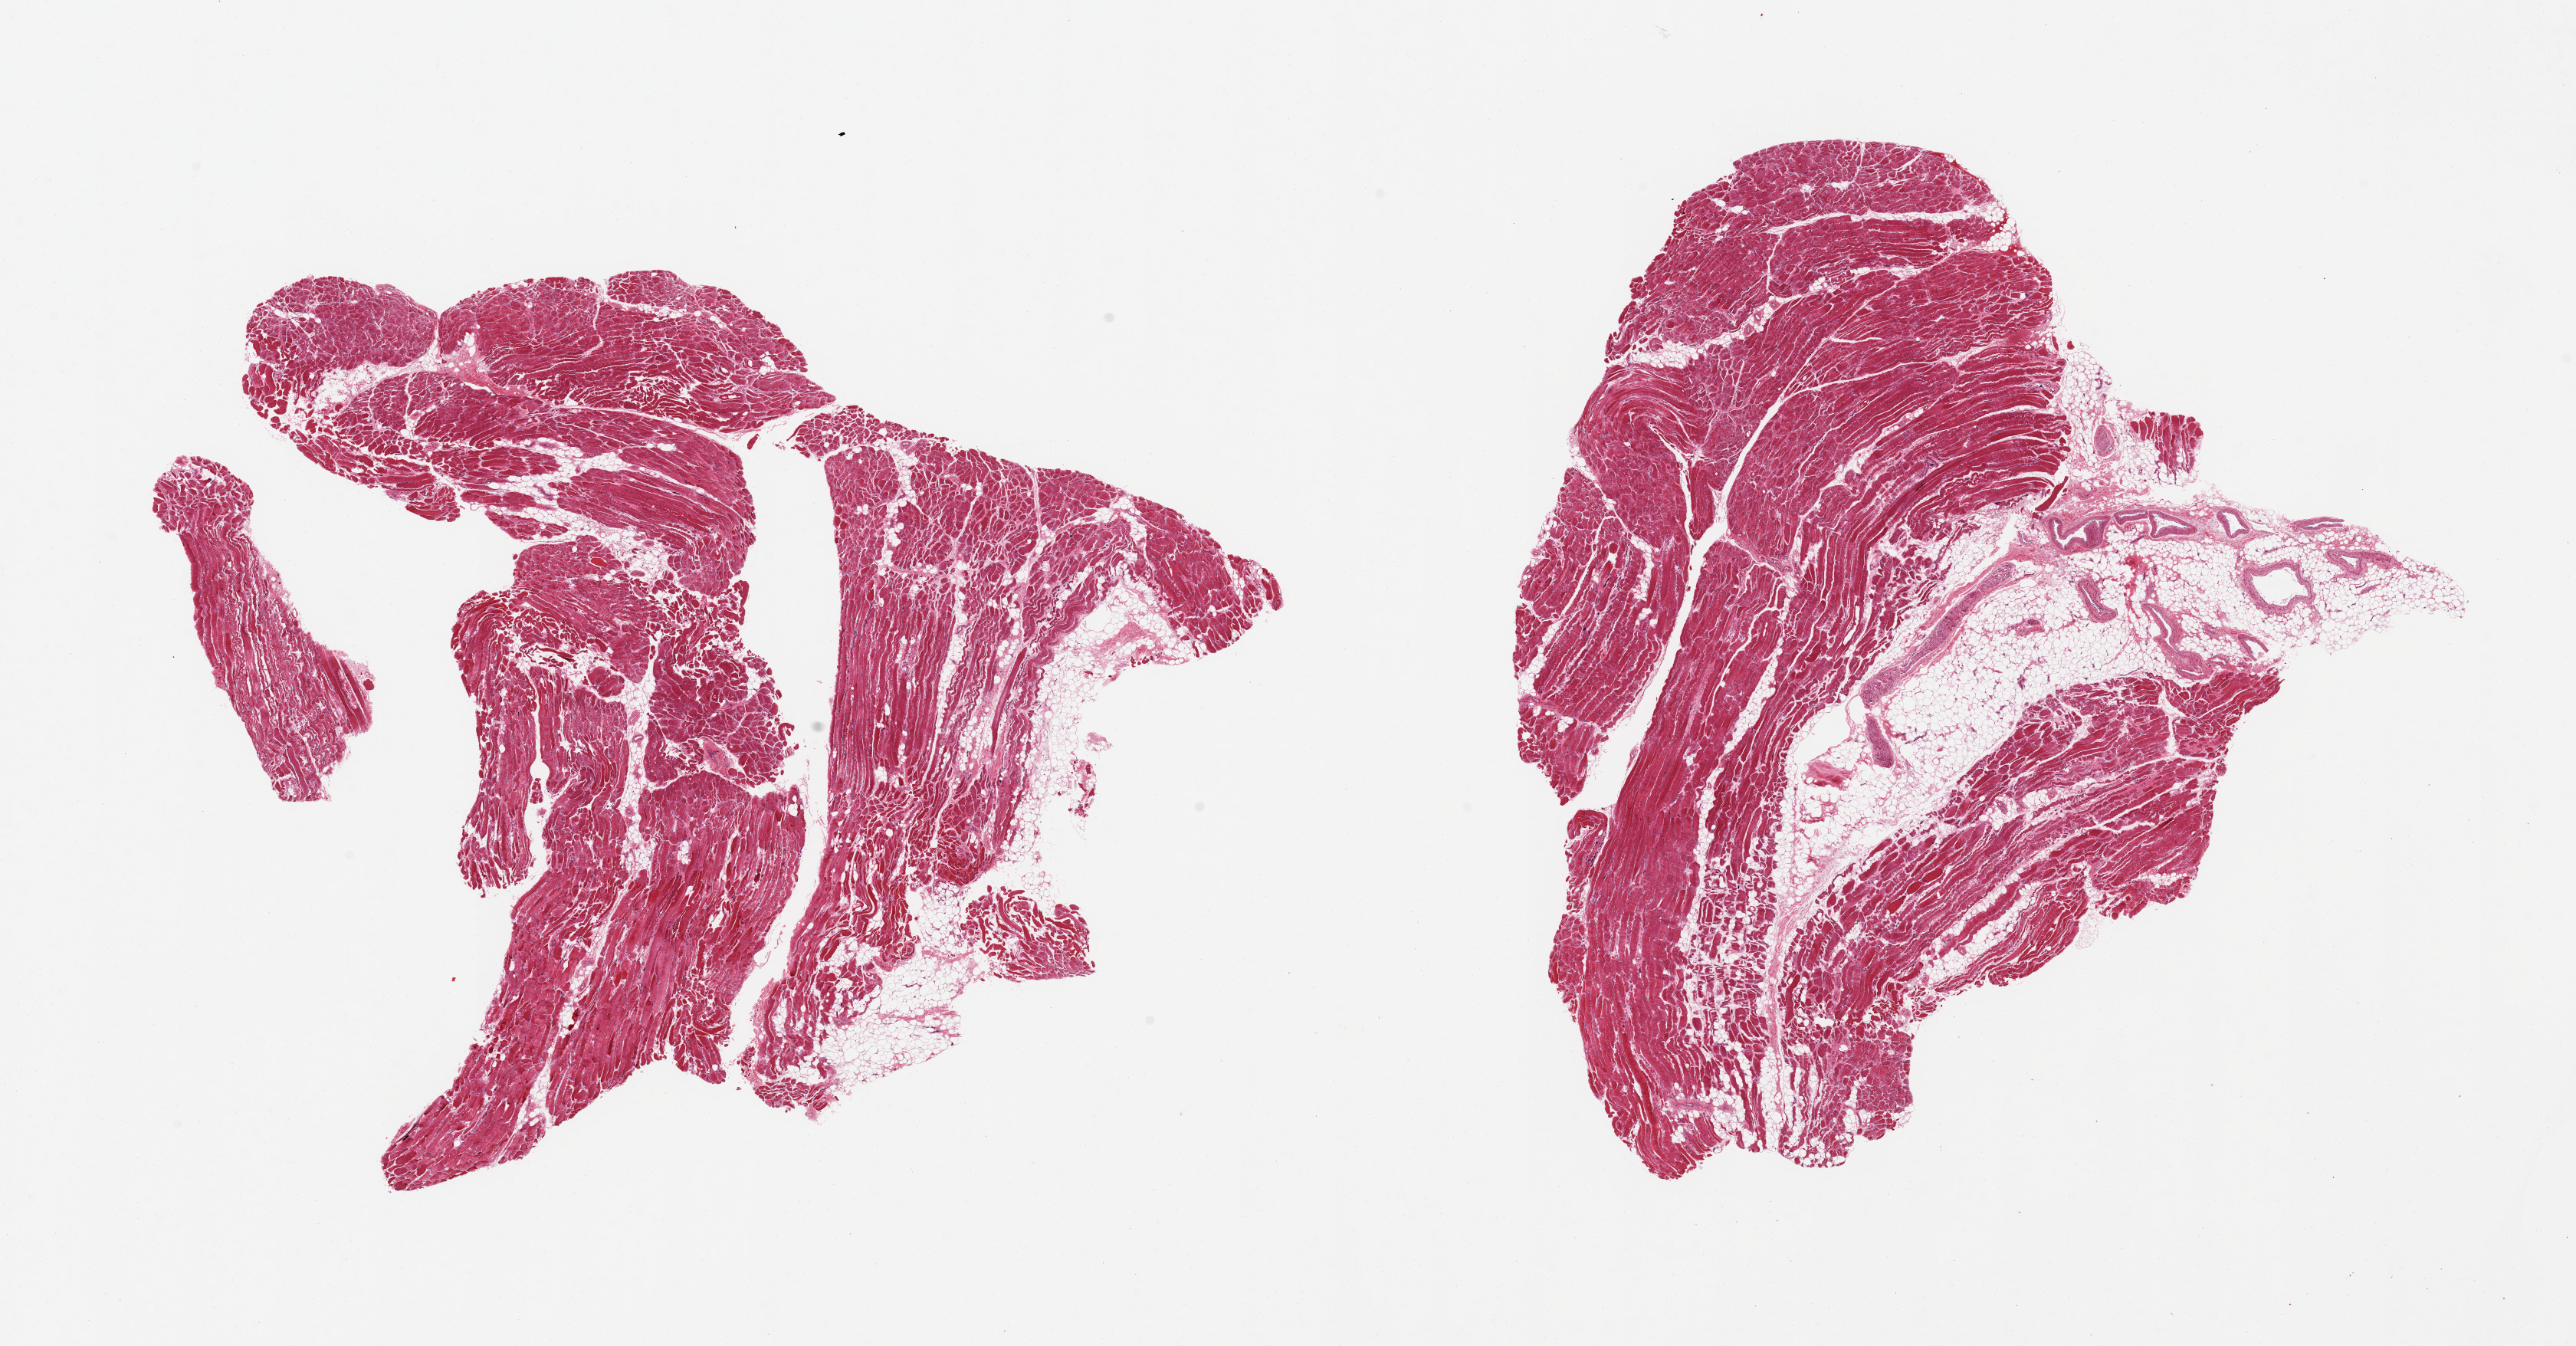
Digitized haematoxylin and eosin-stained section — shown as a low-resolution overview of the whole scanned area (about 26.6 x 13.9 mm). PAXgene-fixed paraffin-embedded (PFPE) section. Section of skeletal muscle (target tissue). Tissue donor sample. Female donor.
* reviewer comment on this tissue sample: 2 pieces; moderate atrophy, 30 & 10% internal fat